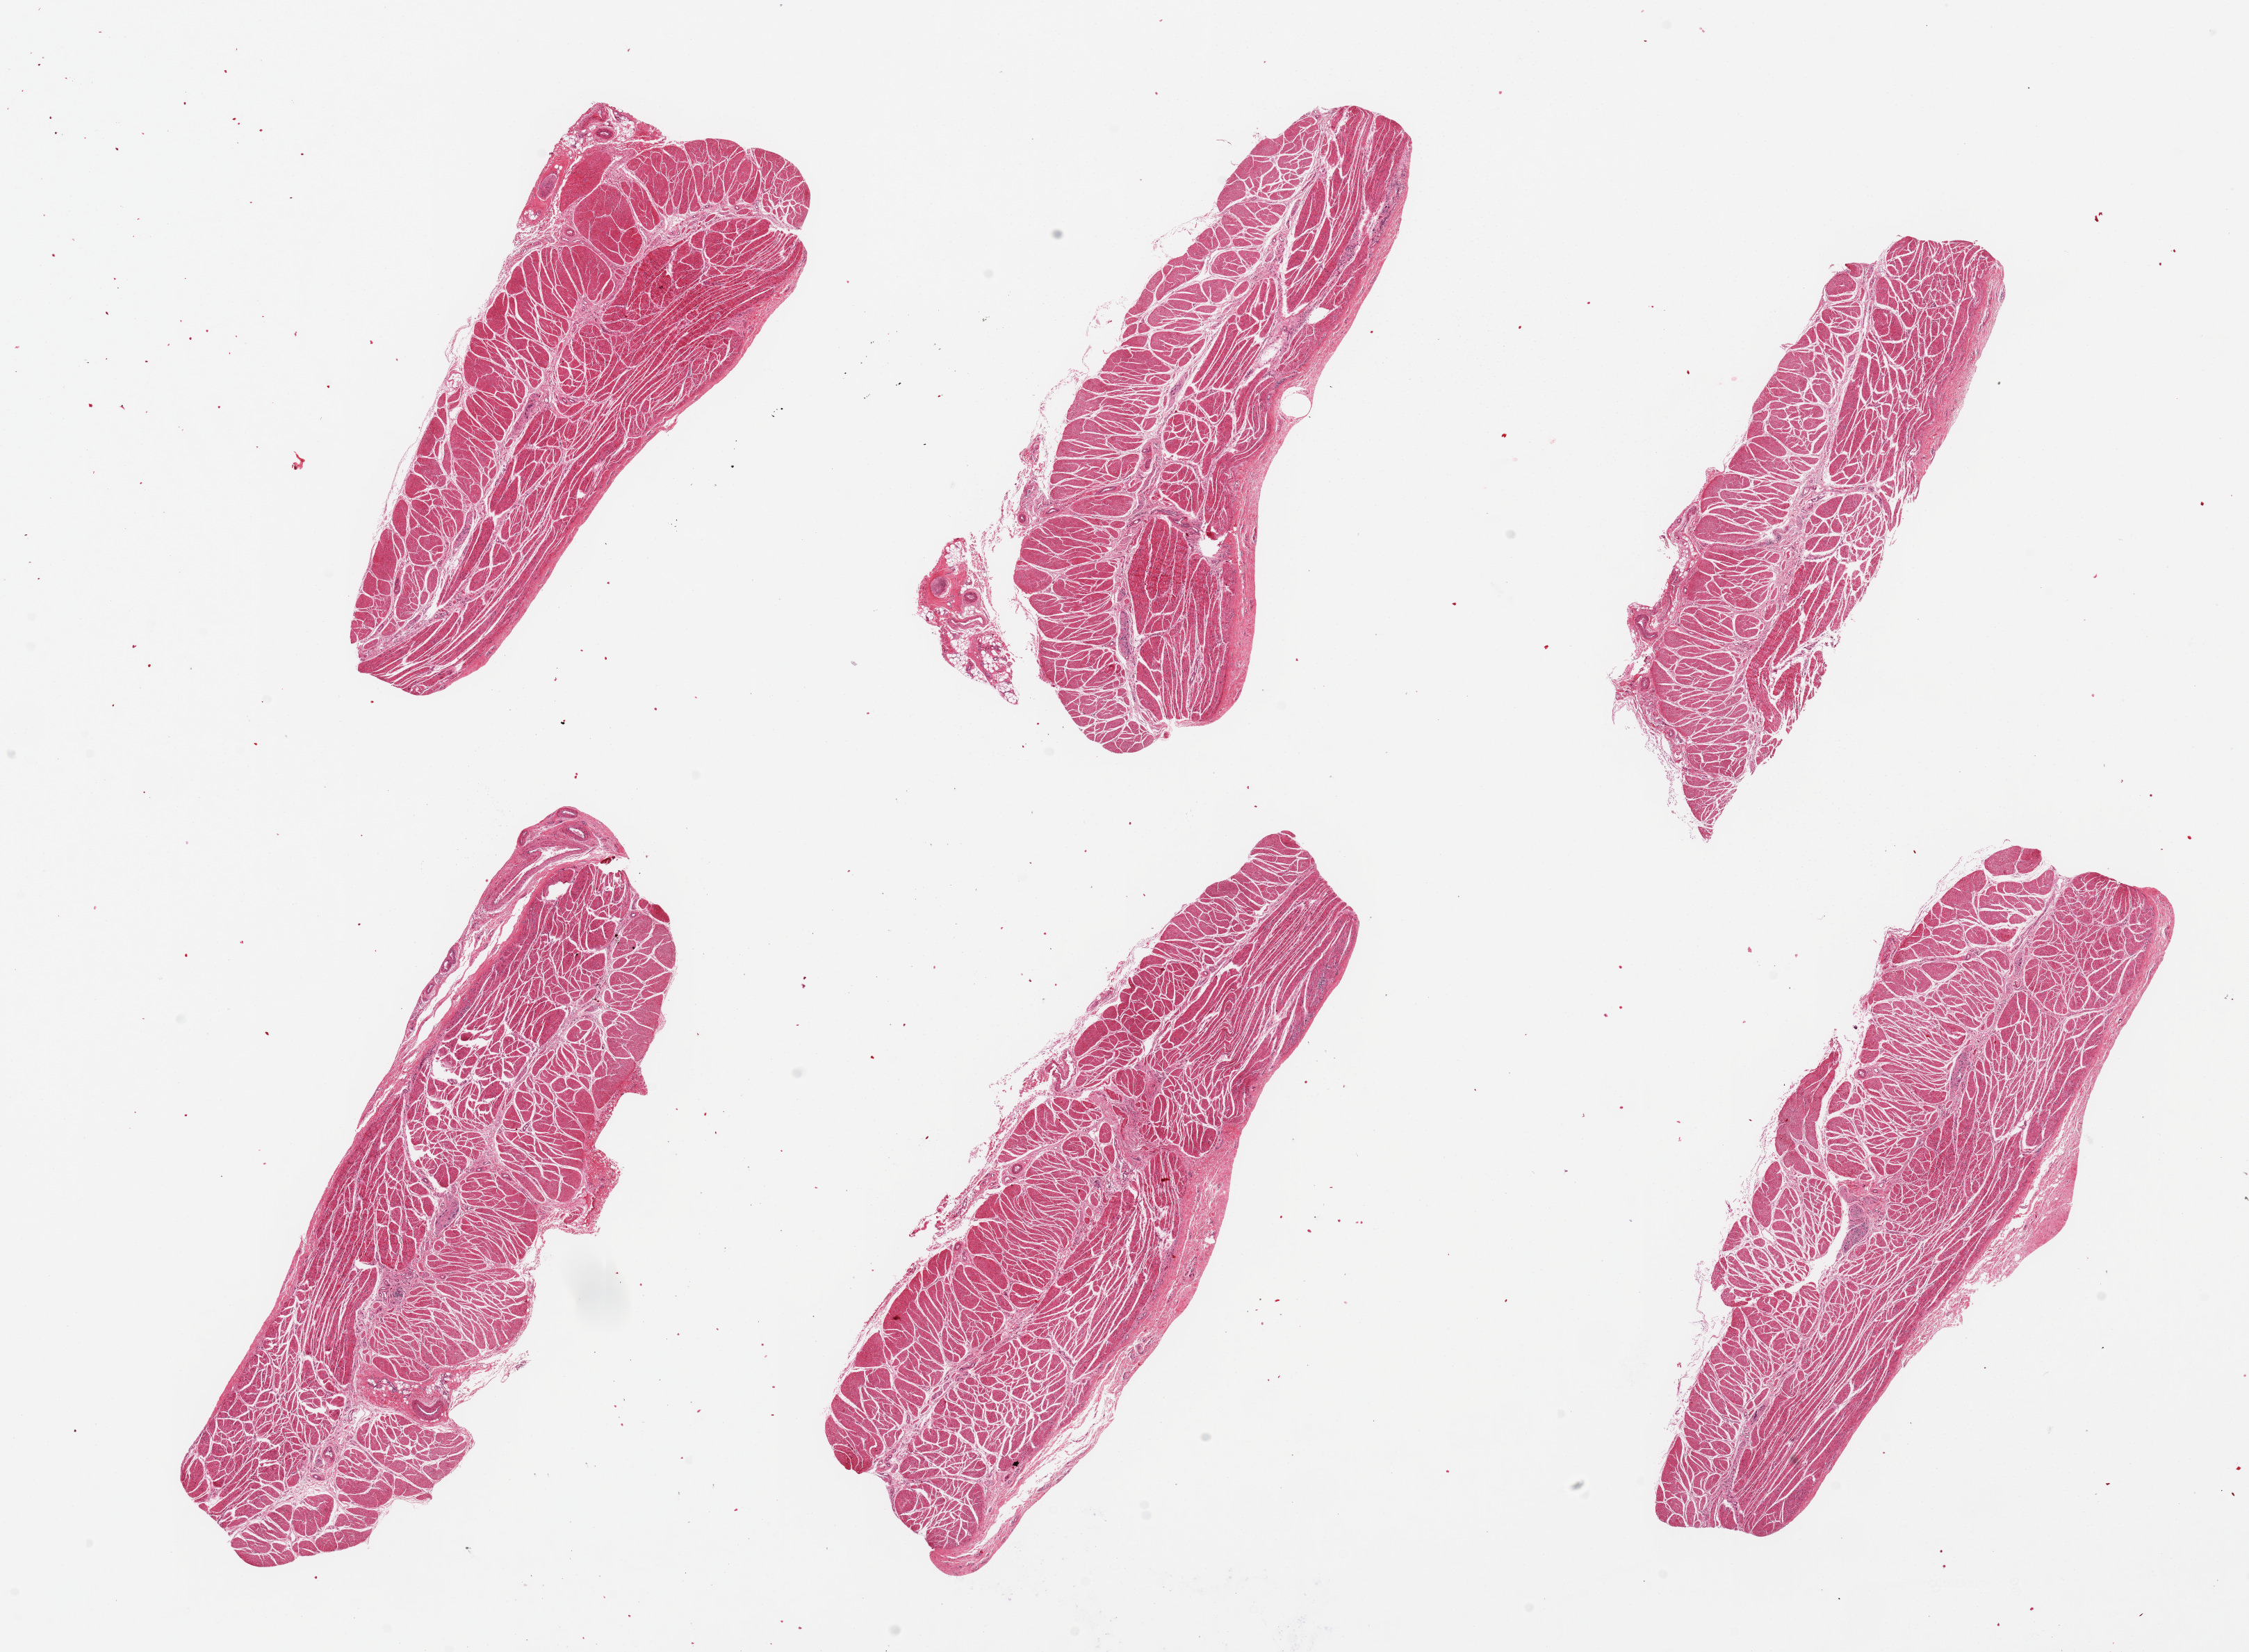
Whole-slide image, H&E stain, a low-resolution overview of the entire scanned area, about 25.6 x 18.8 mm (acquisition: 20x scan). PAXgene-fixed, paraffin-embedded tissue. Section of esophageal muscle (target tissue). Donor tissue sample. Male donor.
Pathologist's review note for this sample: 6 ~8x2mm pieces.